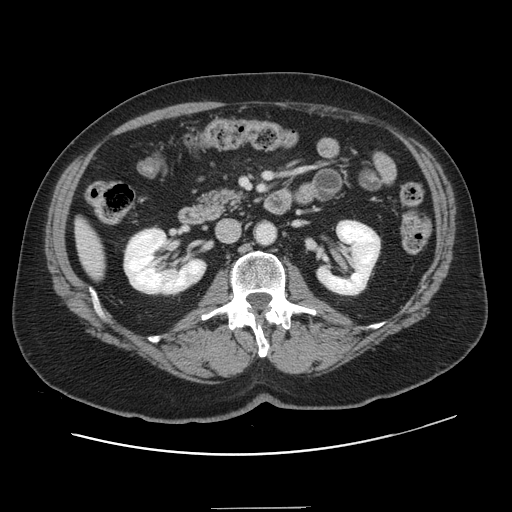
Contrast-enhanced abdominal CT, one axial slice. Position 48 of 143 along the scan axis. 120 kVp. Intravenous contrast given. Soft-tissue window (W 400 / L 40 HU). 2.5 mm slice thickness. 512 × 512 image matrix, field of view 402 × 402 mm. Male patient, age 62 years. Case-level facts recorded for this patient, not image findings: diagnosis: colorectal cancer liver metastases, imaged before liver resection; multiple liver metastases: yes; largest metastasis: 2.7 cm; disease in both lobes: no.
Structures marked on this image (expert manual segmentation):
- liver: bounding box <77,223,104,276> (left, top, right, bottom; pixels)